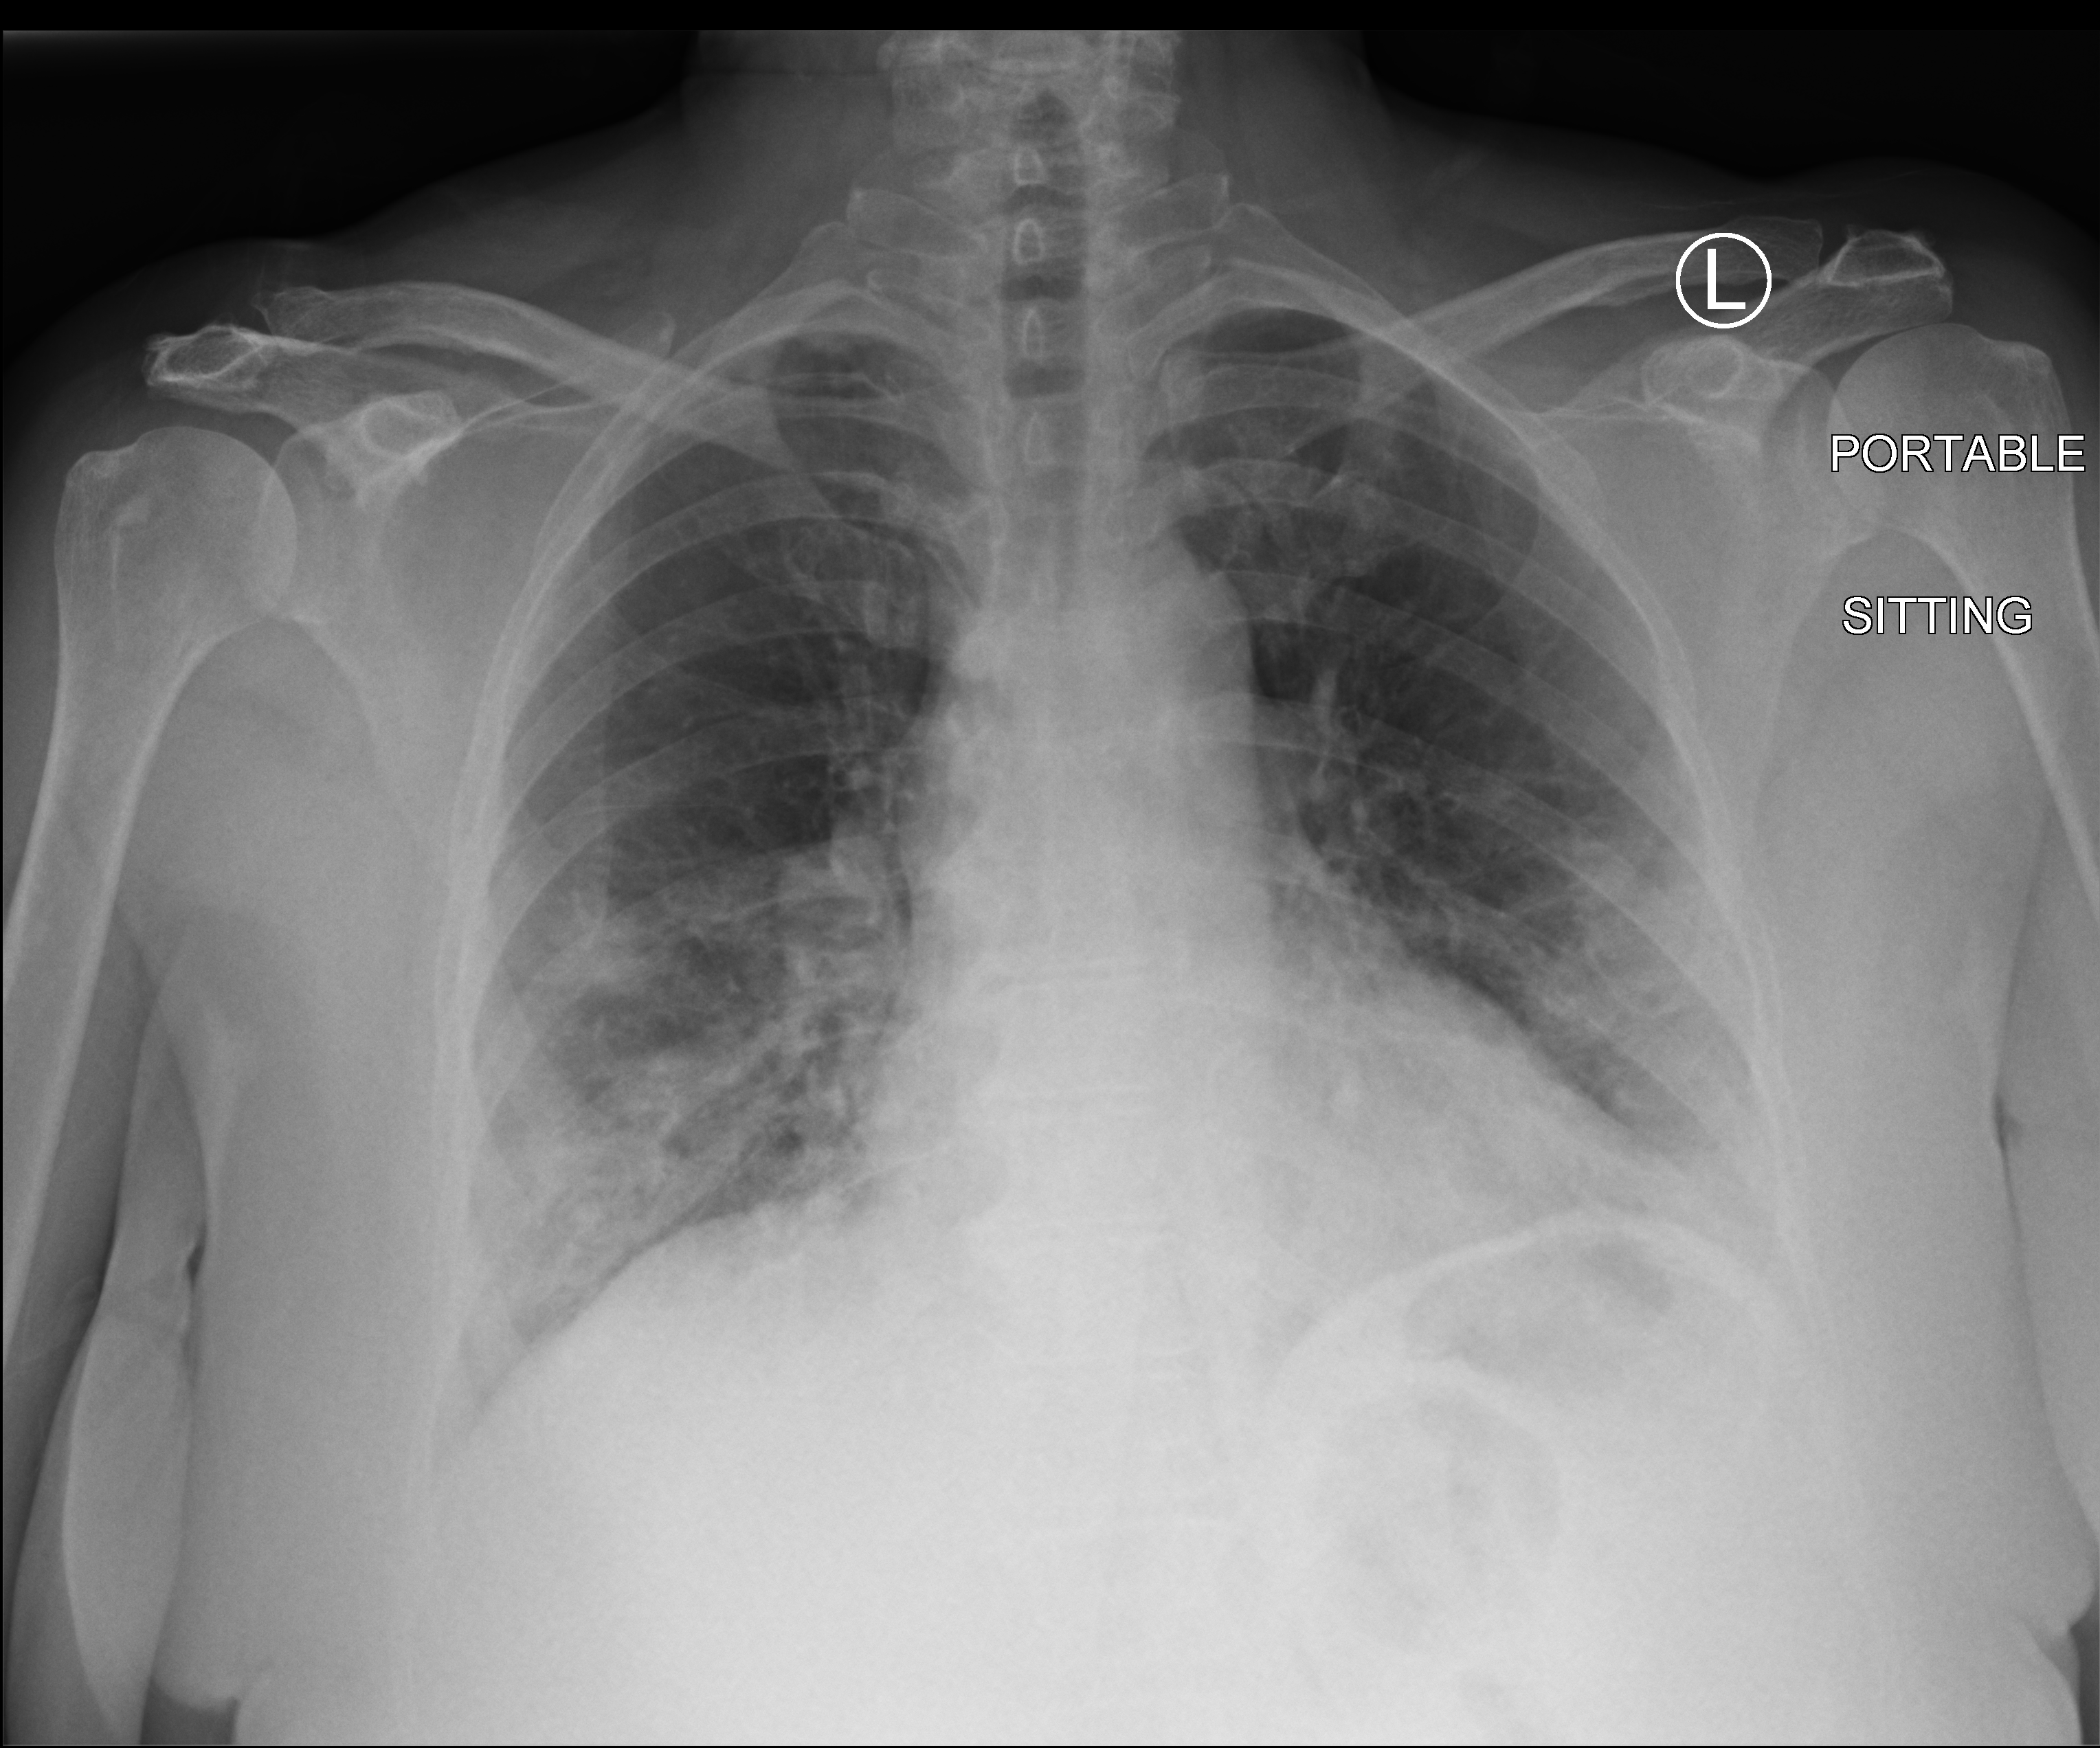
Portable chest radiograph, anteroposterior (AP) projection. Patient hospitalised with COVID-19; female, aged 60–74 years.
Admission-level facts for this patient (not findings on this image; timing relative to this image not recorded): COPD (admission record): no; admitted to intensive care during this hospital stay: no.